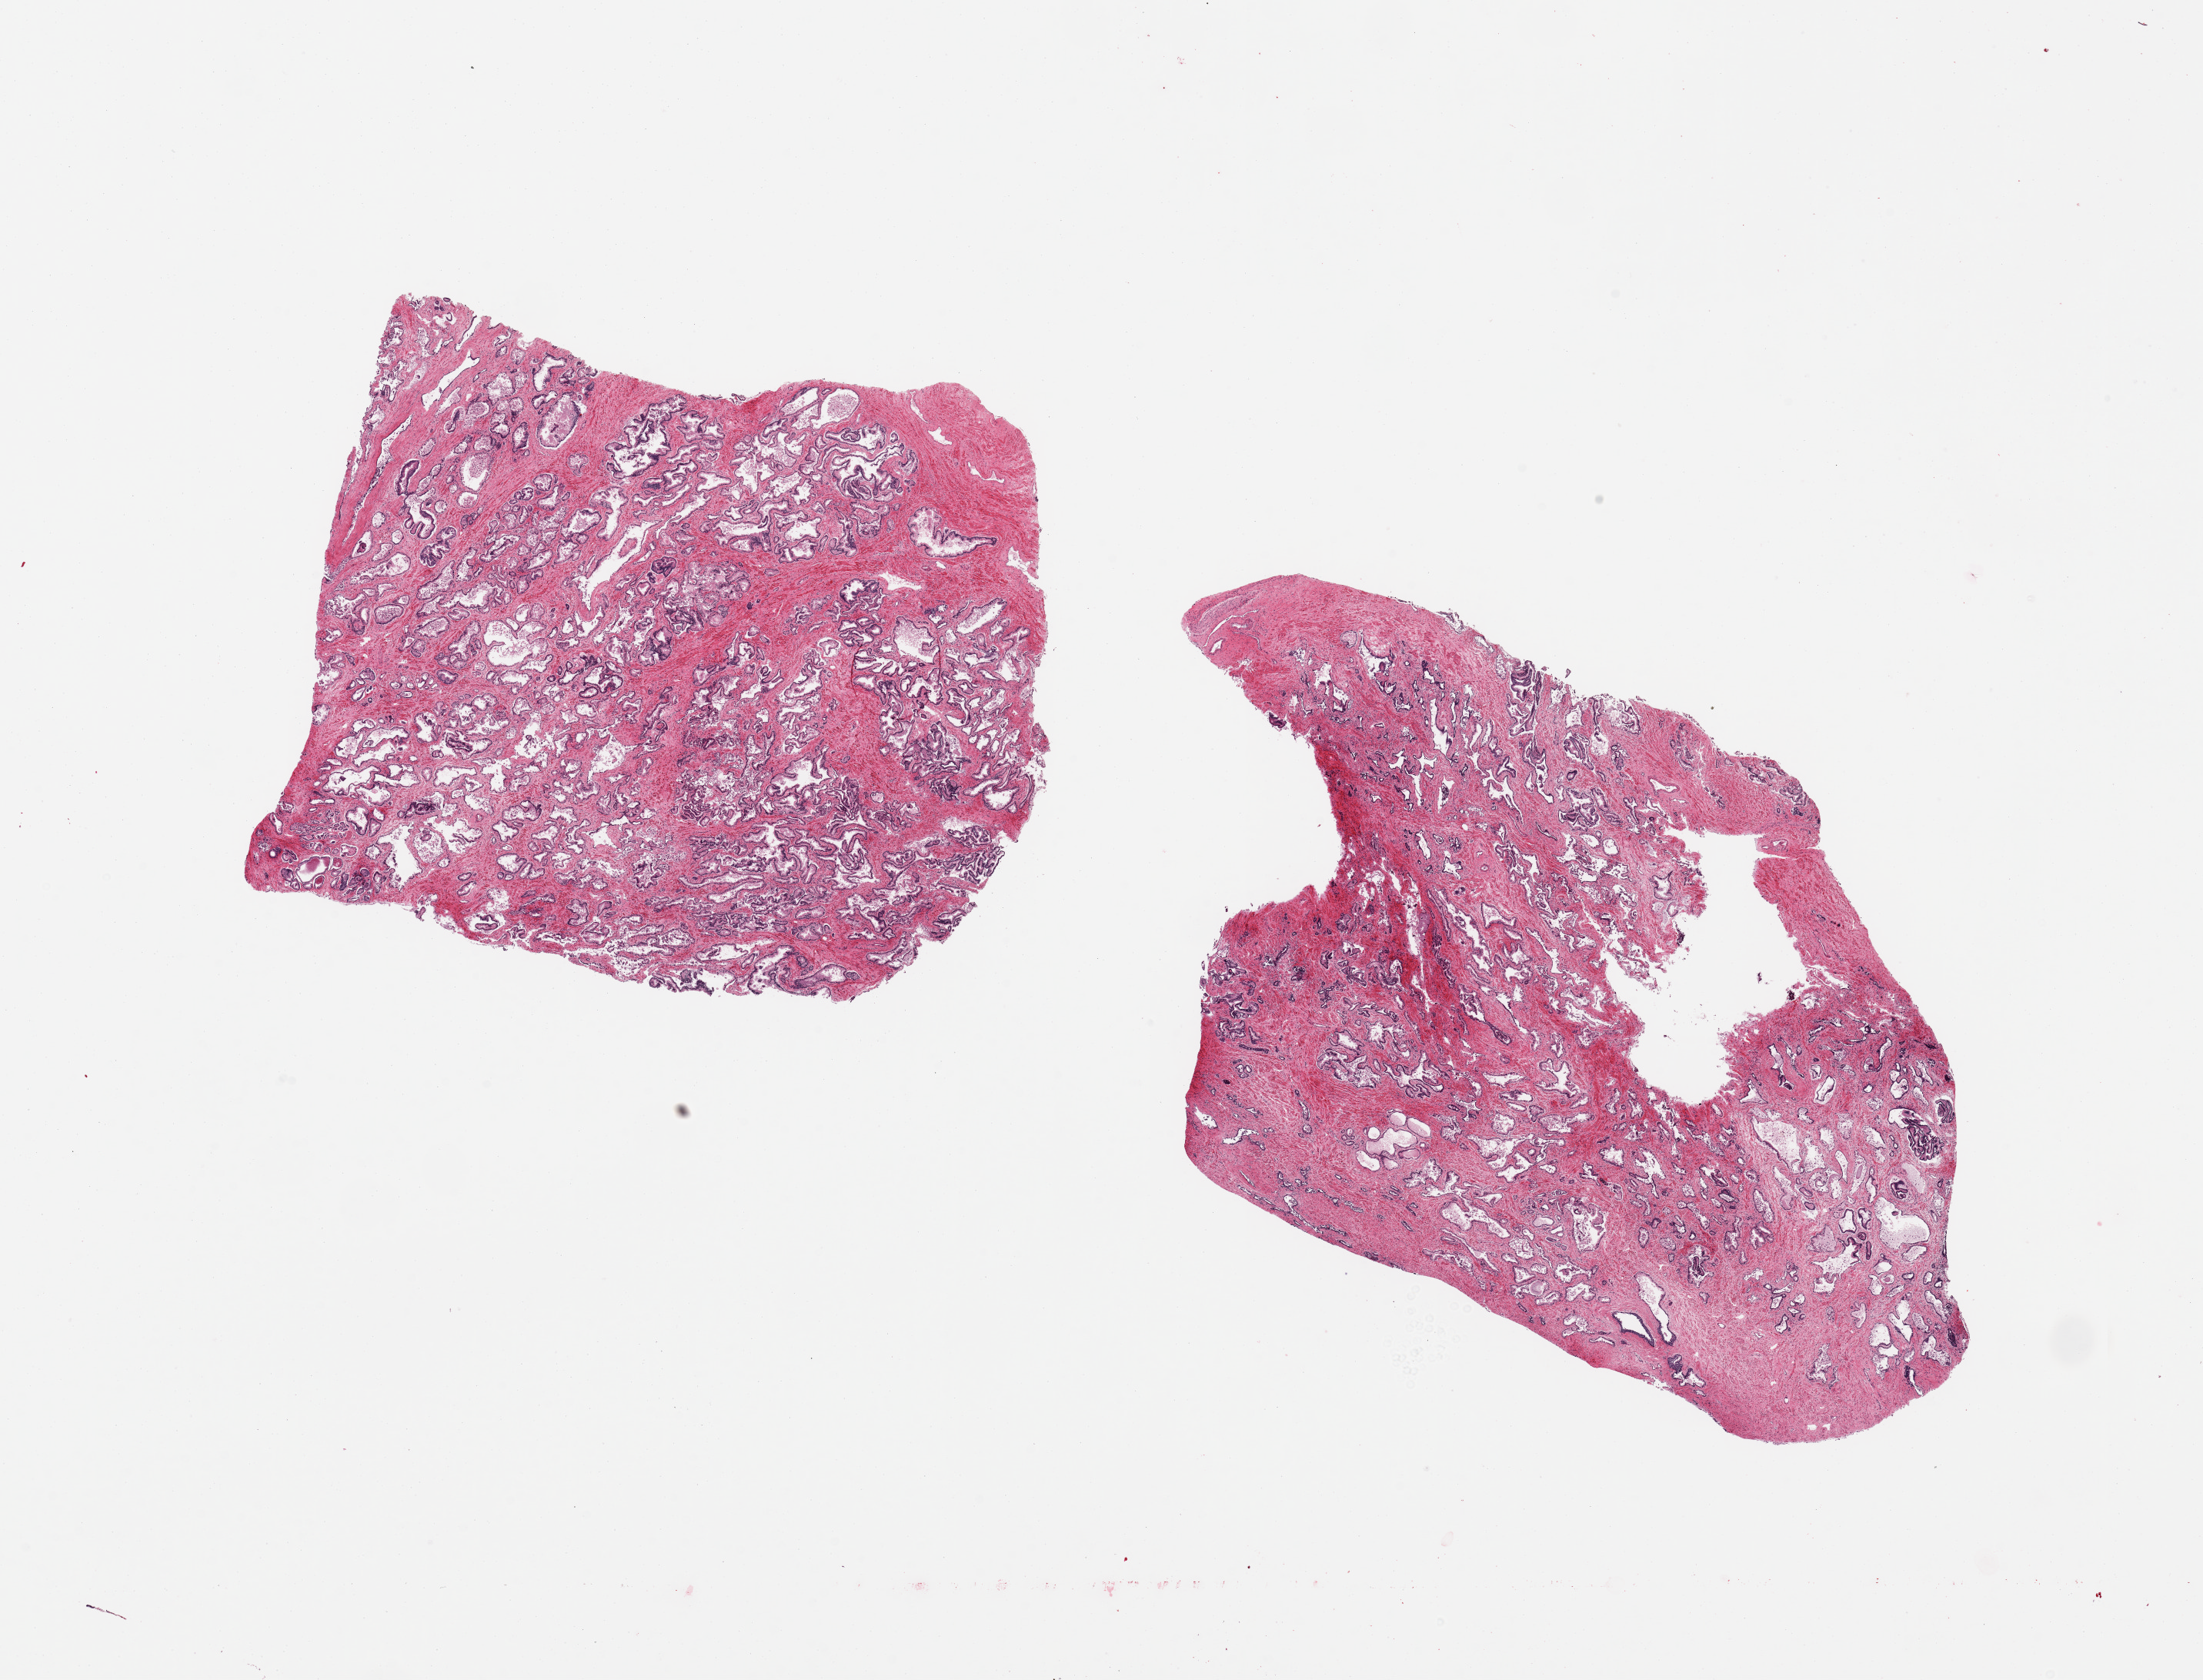
Haematoxylin and eosin whole-slide image, brightfield, whole scanned area (about 22.6 x 17.3 mm) shown as a low-resolution overview; PAXgene-fixed, paraffin-embedded tissue; section of prostate (target tissue); tissue donor sample. Donor: male.
Reviewer comment on this tissue sample: 2 pieces.